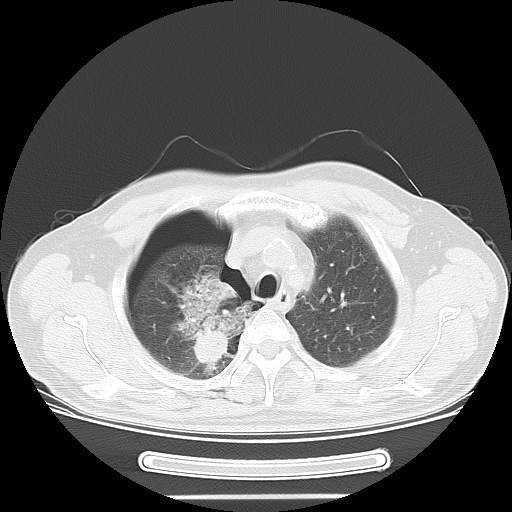
Chest CT, one axial slice. Position 46 of 57 along the scan axis. Reconstruction kernel LUNG. Lung window (W 1500 / L -600 HU). 5 mm slice thickness. 512 × 512 image matrix, field of view 376 × 376 mm. Male patient, age 61 years. Case-level facts recorded for this patient, not image findings: clinical TNM (as recorded): T1c N3 M1b.
Annotated regions visible in this slice (rectangle marked by the reading radiologist):
- lung tumour (recorded histology: adenocarcinoma): bounding box (x1, y1, x2, y2) in pixels: (163, 265, 257, 376)